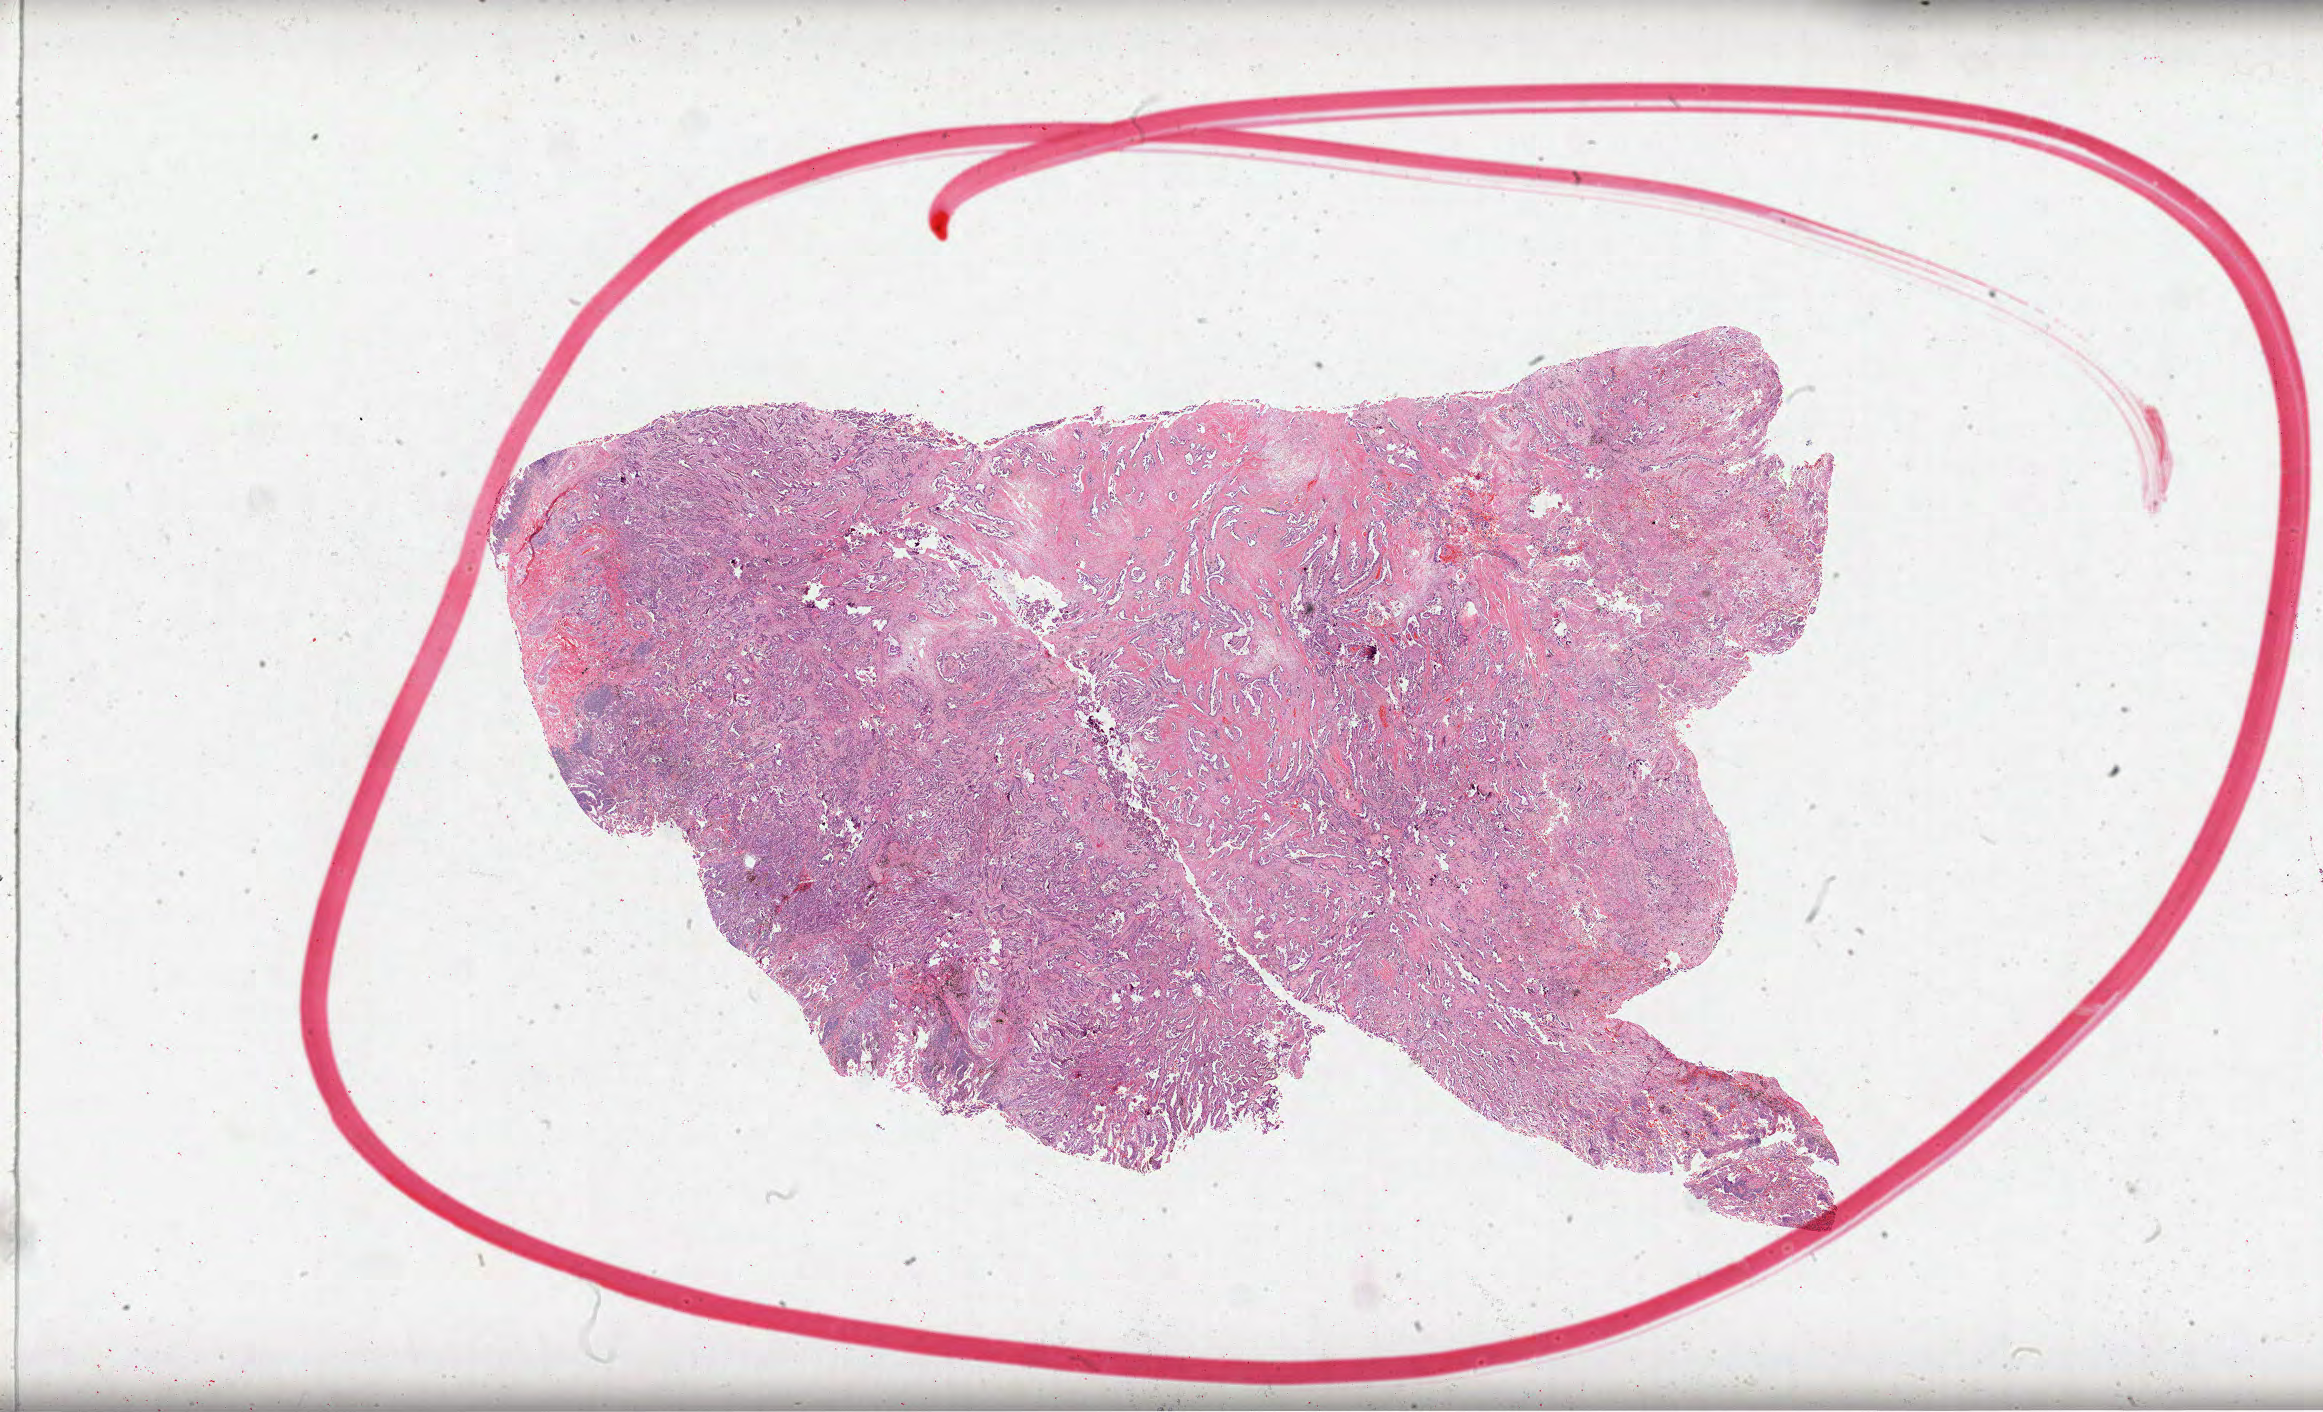
Whole-slide histology image, Hematoxylin and eosin (H&E) stained, low-resolution overview of the scanned area, about 37.5 x 22.8 mm (slide scanned at 40x), formalin-fixed paraffin-embedded (FFPE) diagnostic section, lung, primary tumour sample. Patient: male, age at initial diagnosis 46 years.
AJCC pathologic stage: IIA. Histologic diagnosis: Adenocarcinoma, NOS.